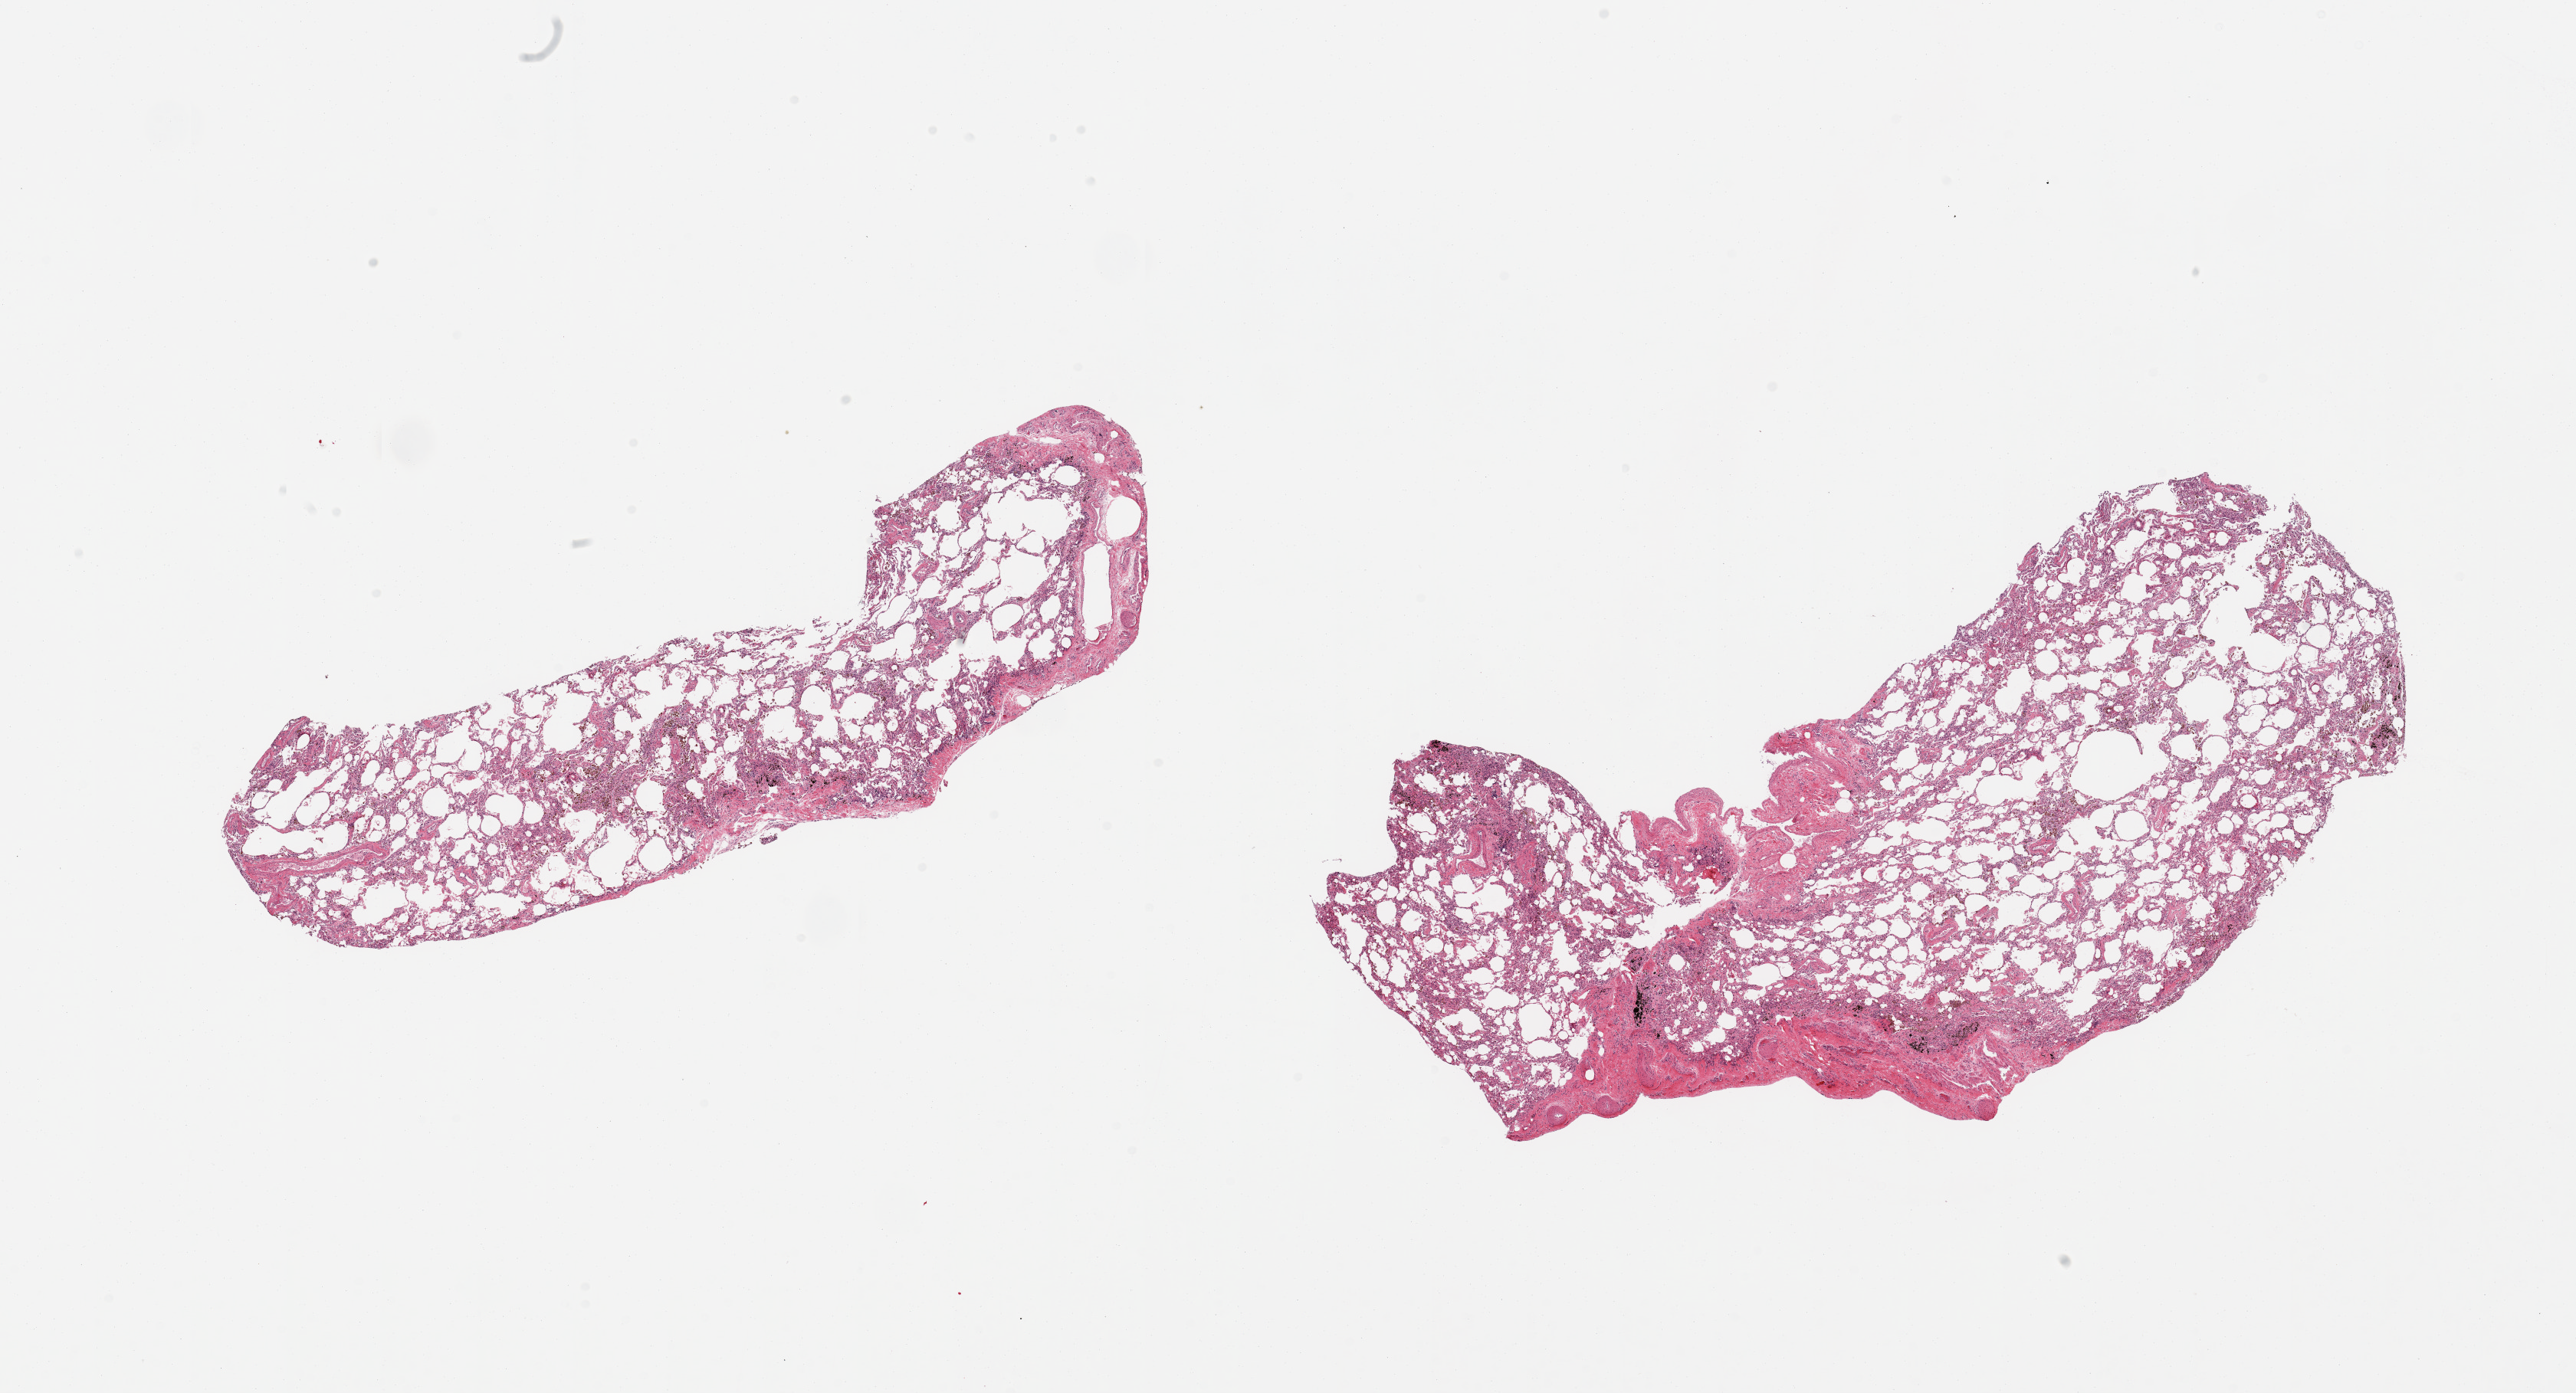
Digitized hematoxylin and eosin (H&E)-stained section — low-resolution overview of the scanned area, about 26.6 x 14.4 mm; PAXgene-fixed paraffin-embedded (PFPE) section; target tissue: lung; tissue donor sample. Donor: male.
Reviewer comment on this tissue sample: 2 pieces, minimla congestion.